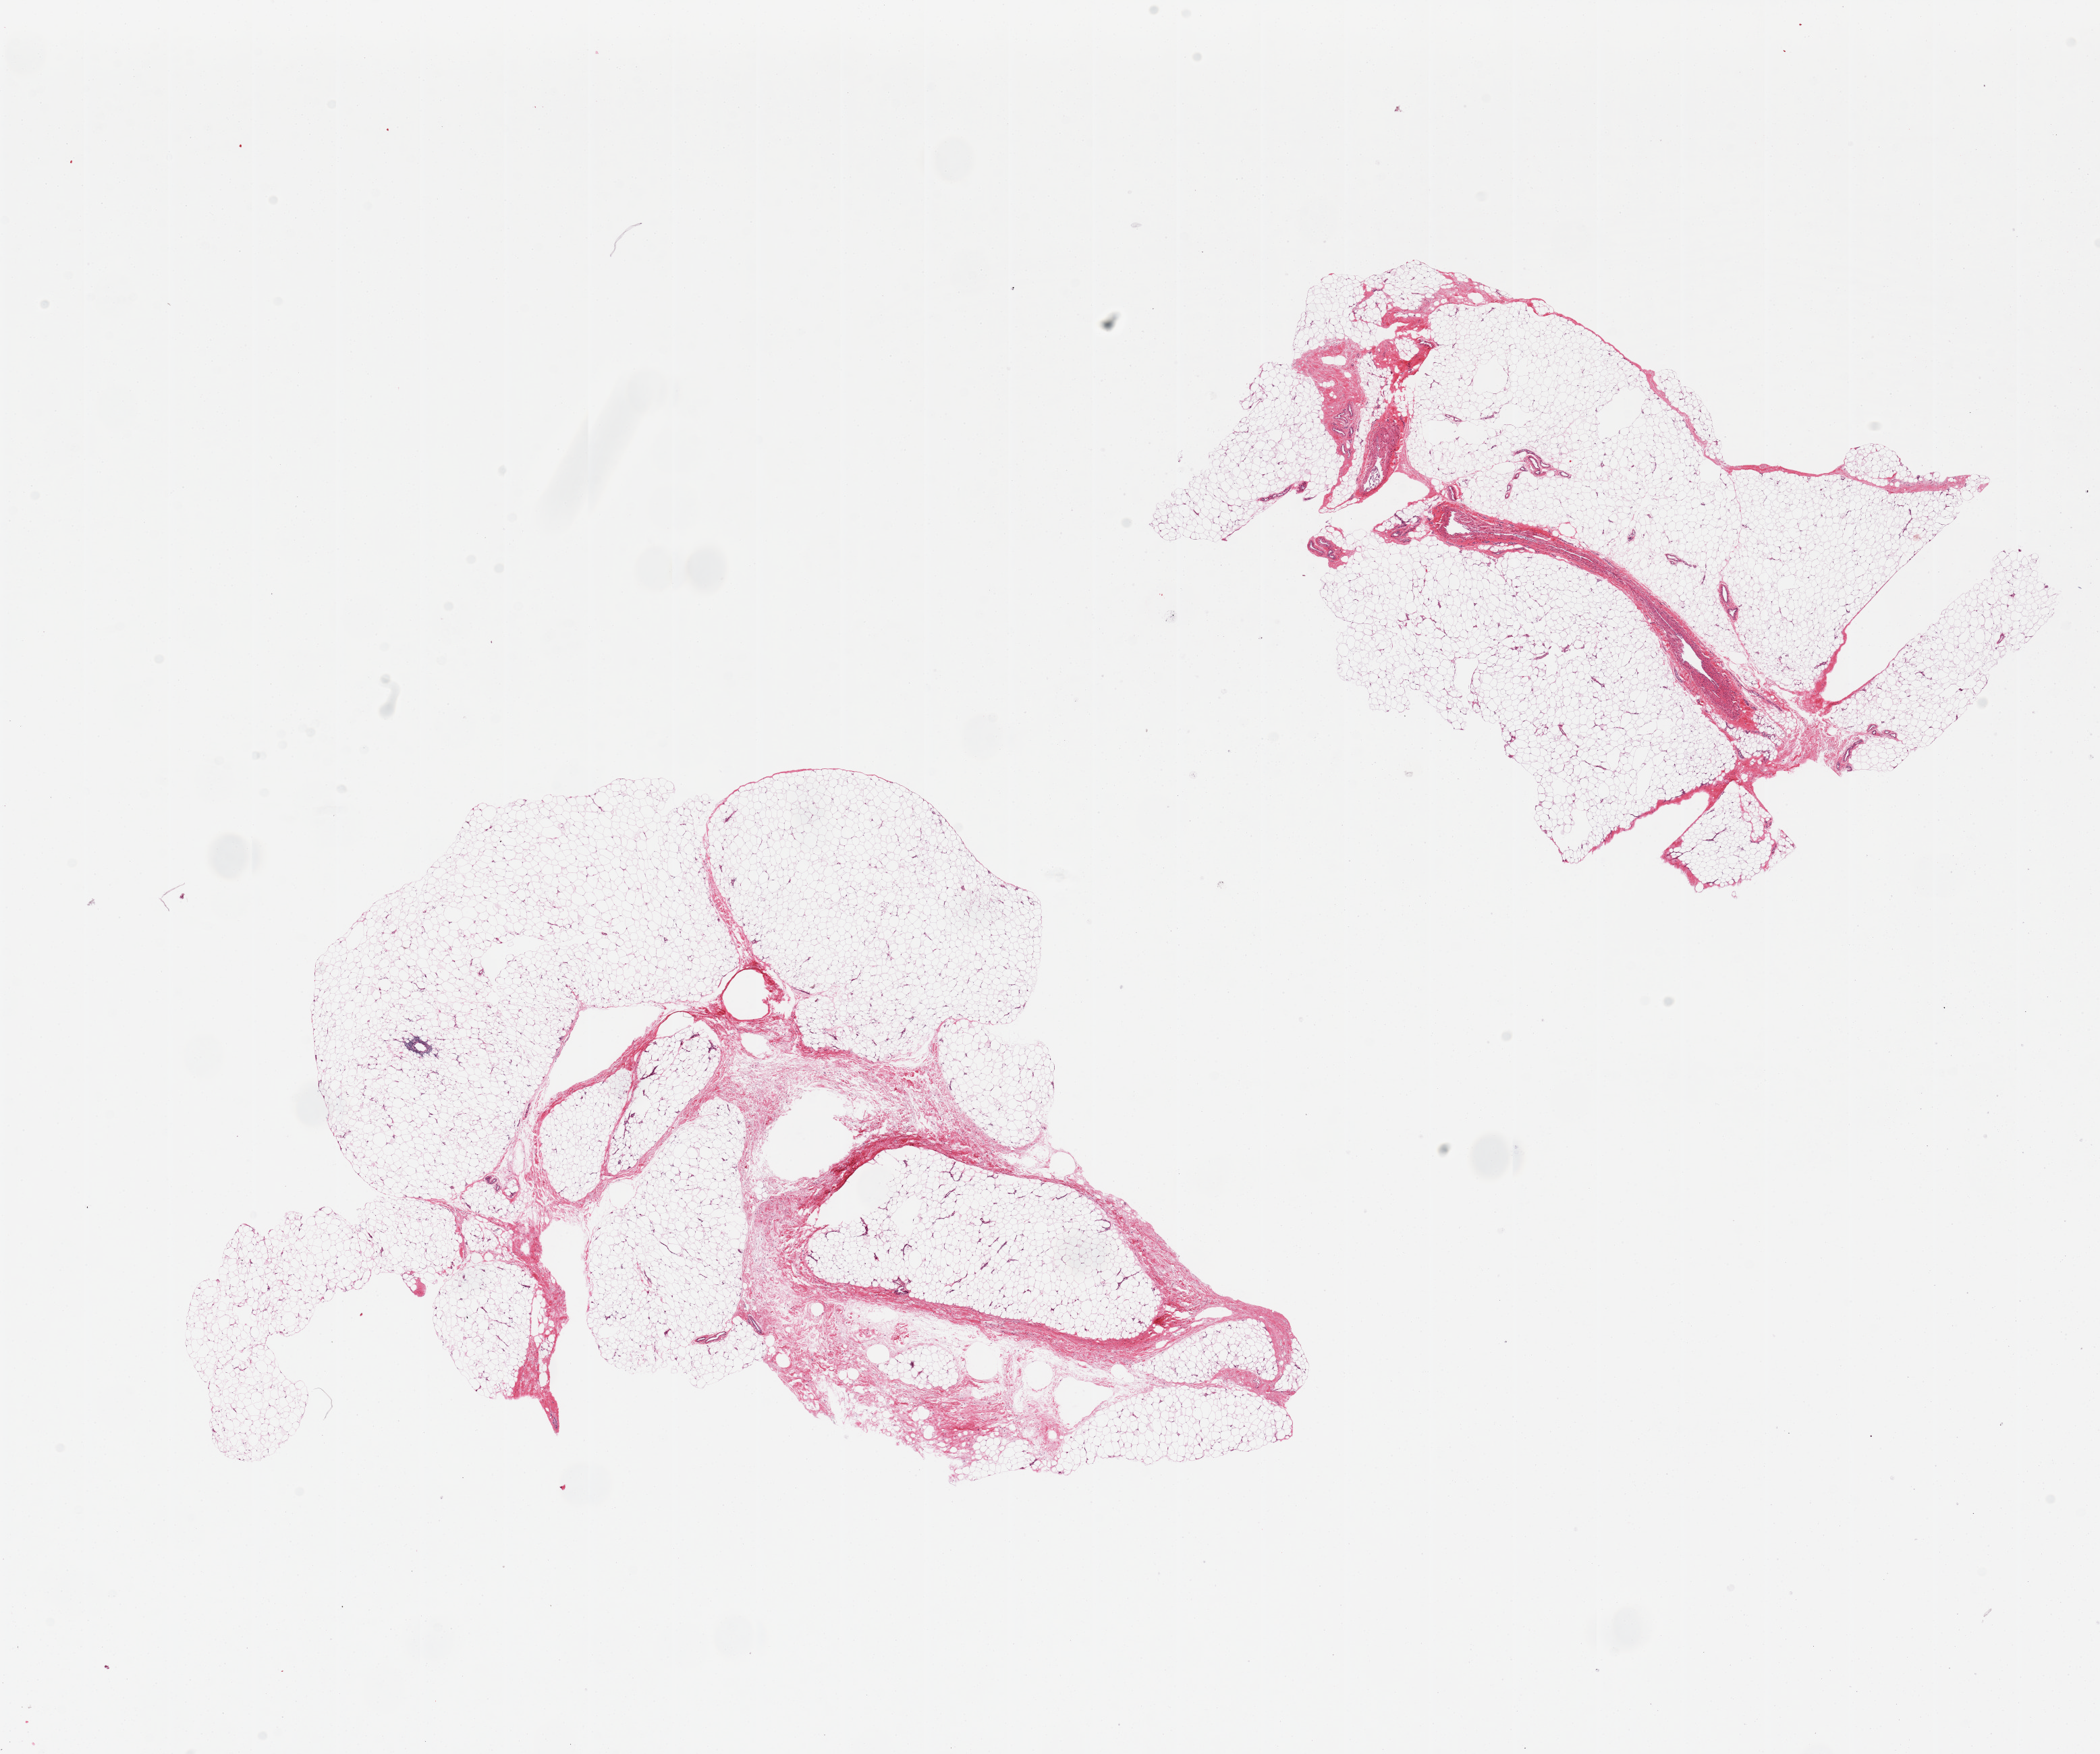
H&E whole-slide image, brightfield, shown as a low-resolution overview of the whole scanned area (about 24.6 x 20.6 mm, from a 20x scan). PAXgene-fixed, paraffin-embedded tissue. Sampled site (target tissue): adipose tissue. Donor tissue sample. Donor: female.
• pathologist's review note for this sample: 2 pieces